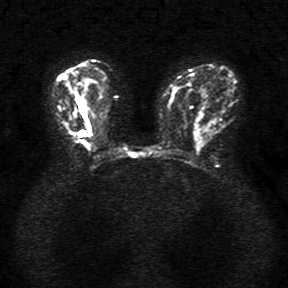
Breast MRI, one axial slice; slice 15 of 34 in the series (ordered by position); diffusion-weighted series; image 2 of 4 stored at this slice position (different b-values; order by instance number); 1.5 T; 5 mm slice thickness; 288 × 288 image matrix, field of view 340 × 340 mm. Female patient.
Structures marked on this image (expert manual segmentation):
- tumour on diffusion-weighted imaging: box from (x=77, y=100) to (x=82, y=112) px